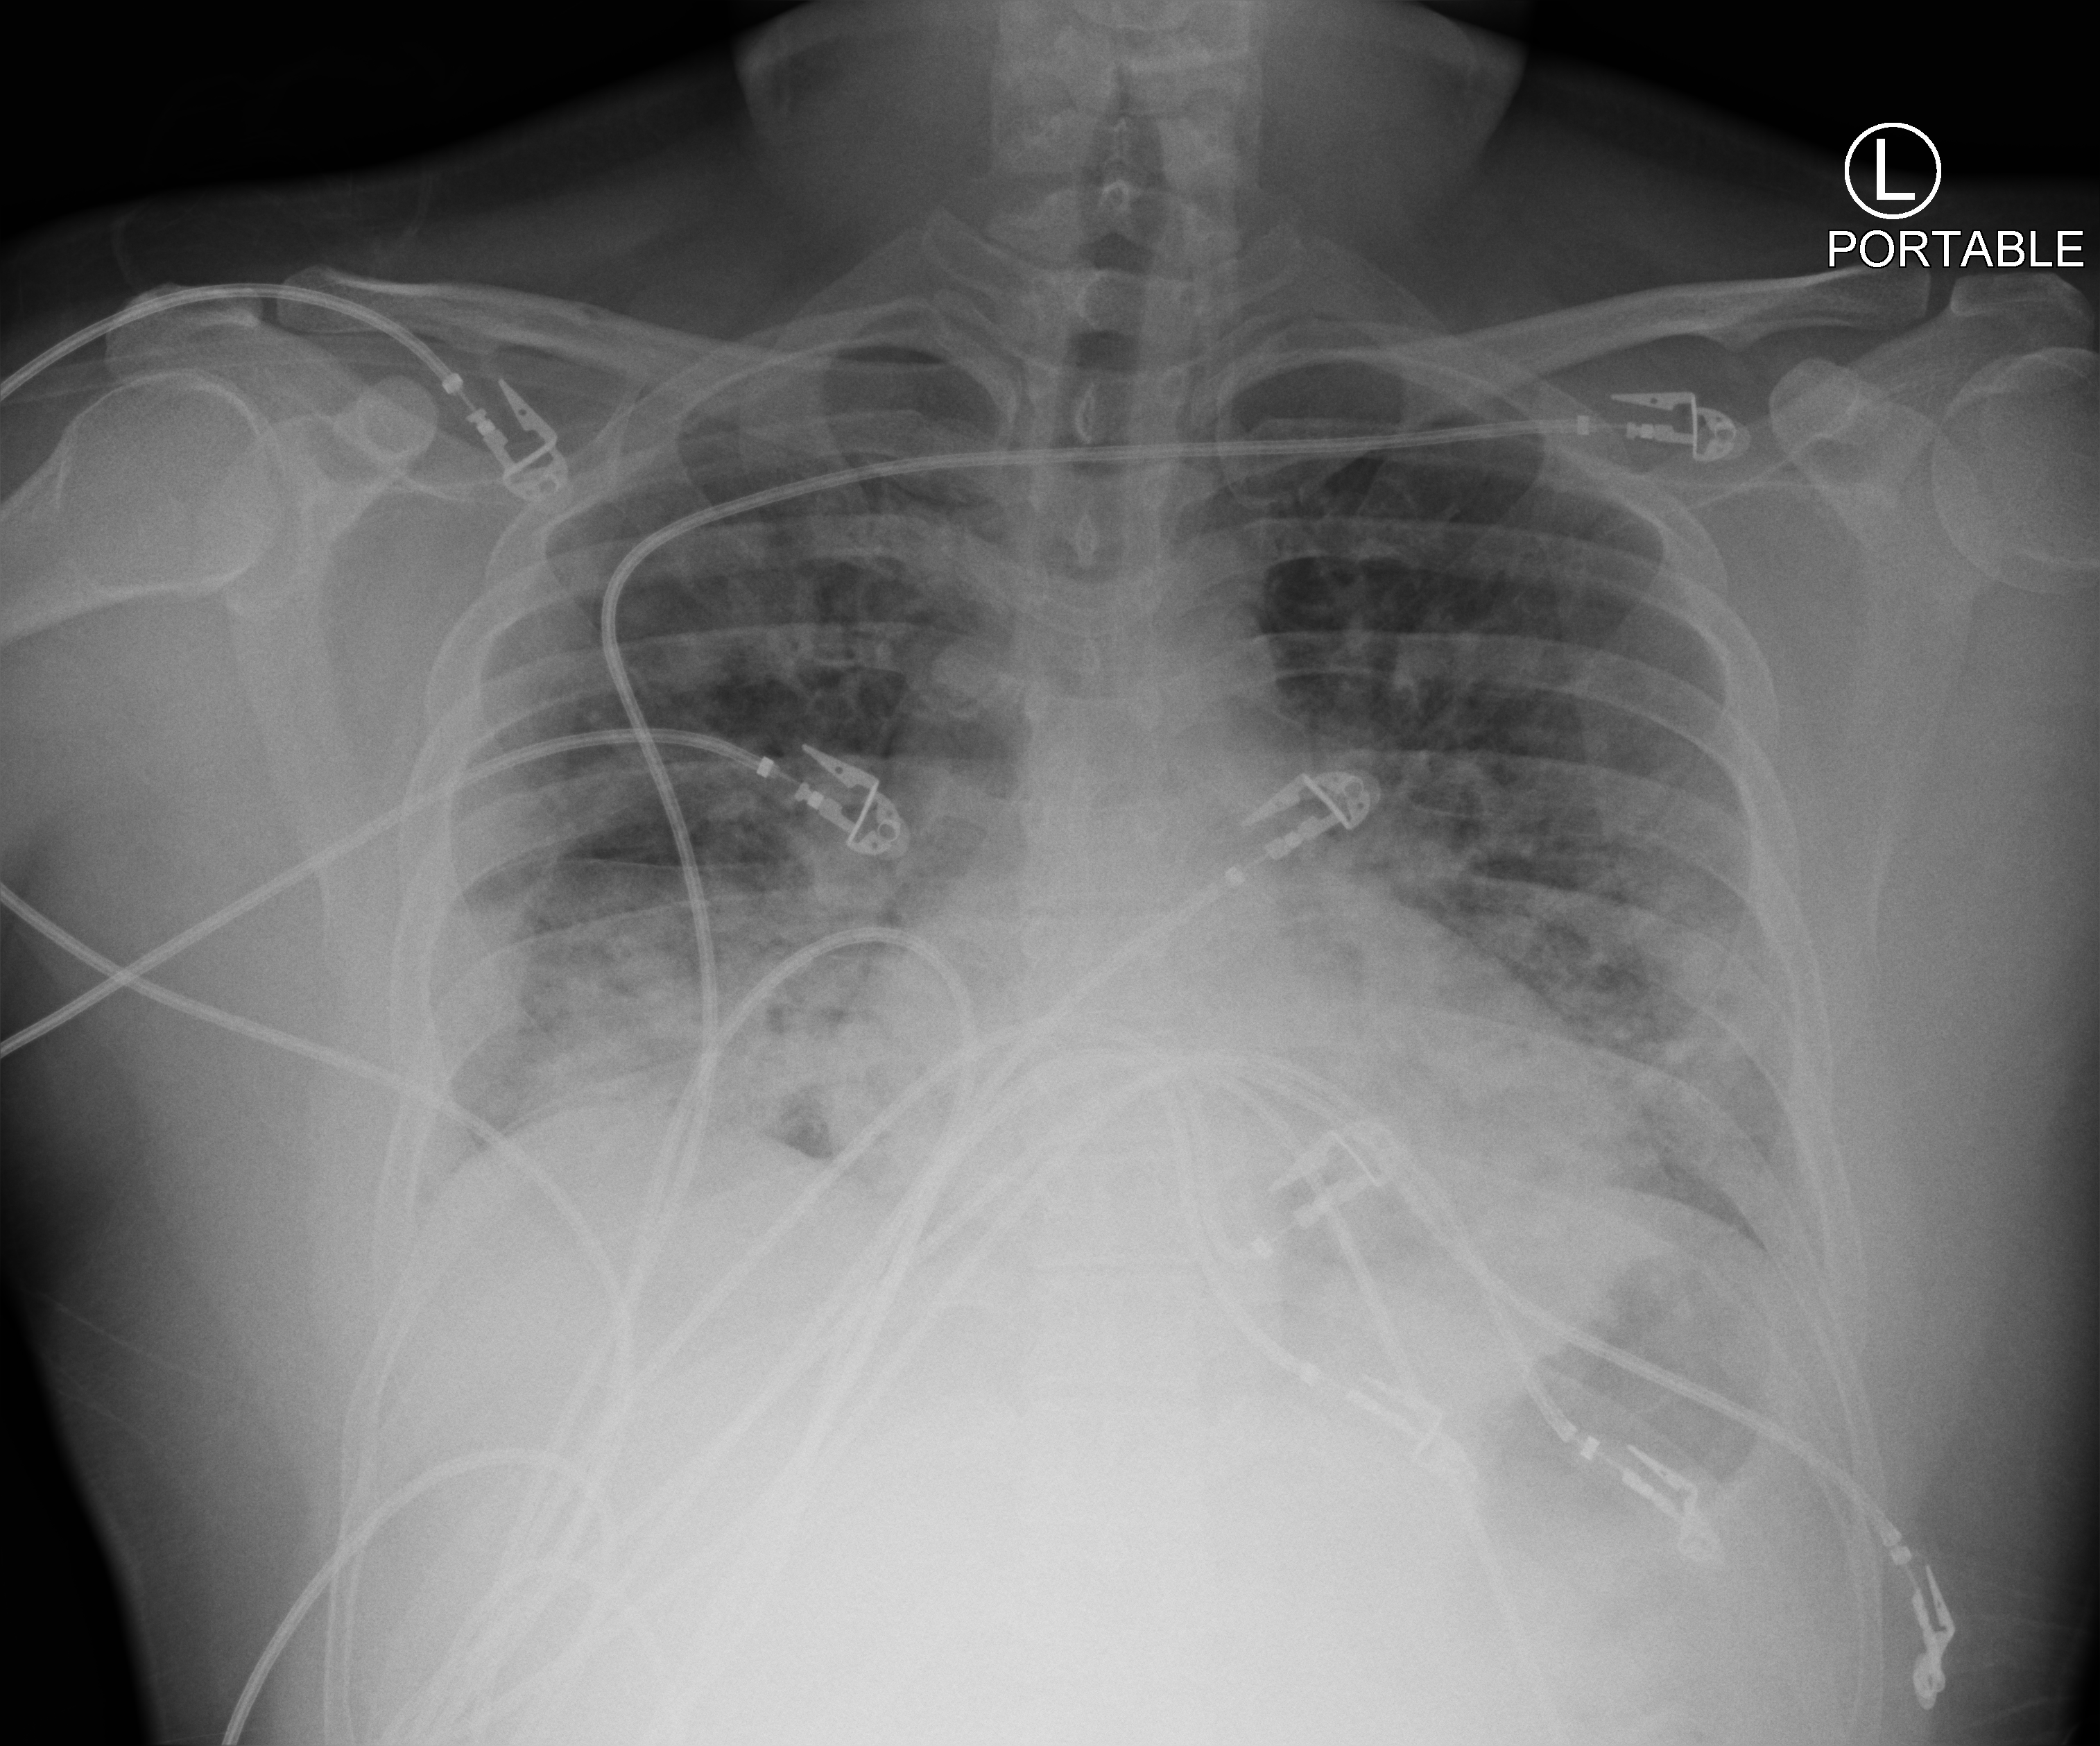
Bedside chest radiograph (computed radiography); anteroposterior (AP) projection. Male patient hospitalised with COVID-19, age 18–59 years.
Hospital-stay facts (about this admission, not read from this image; timing relative to this image not recorded): admitted to intensive care during this hospital stay: no; other chronic lung disease (admission record): yes.